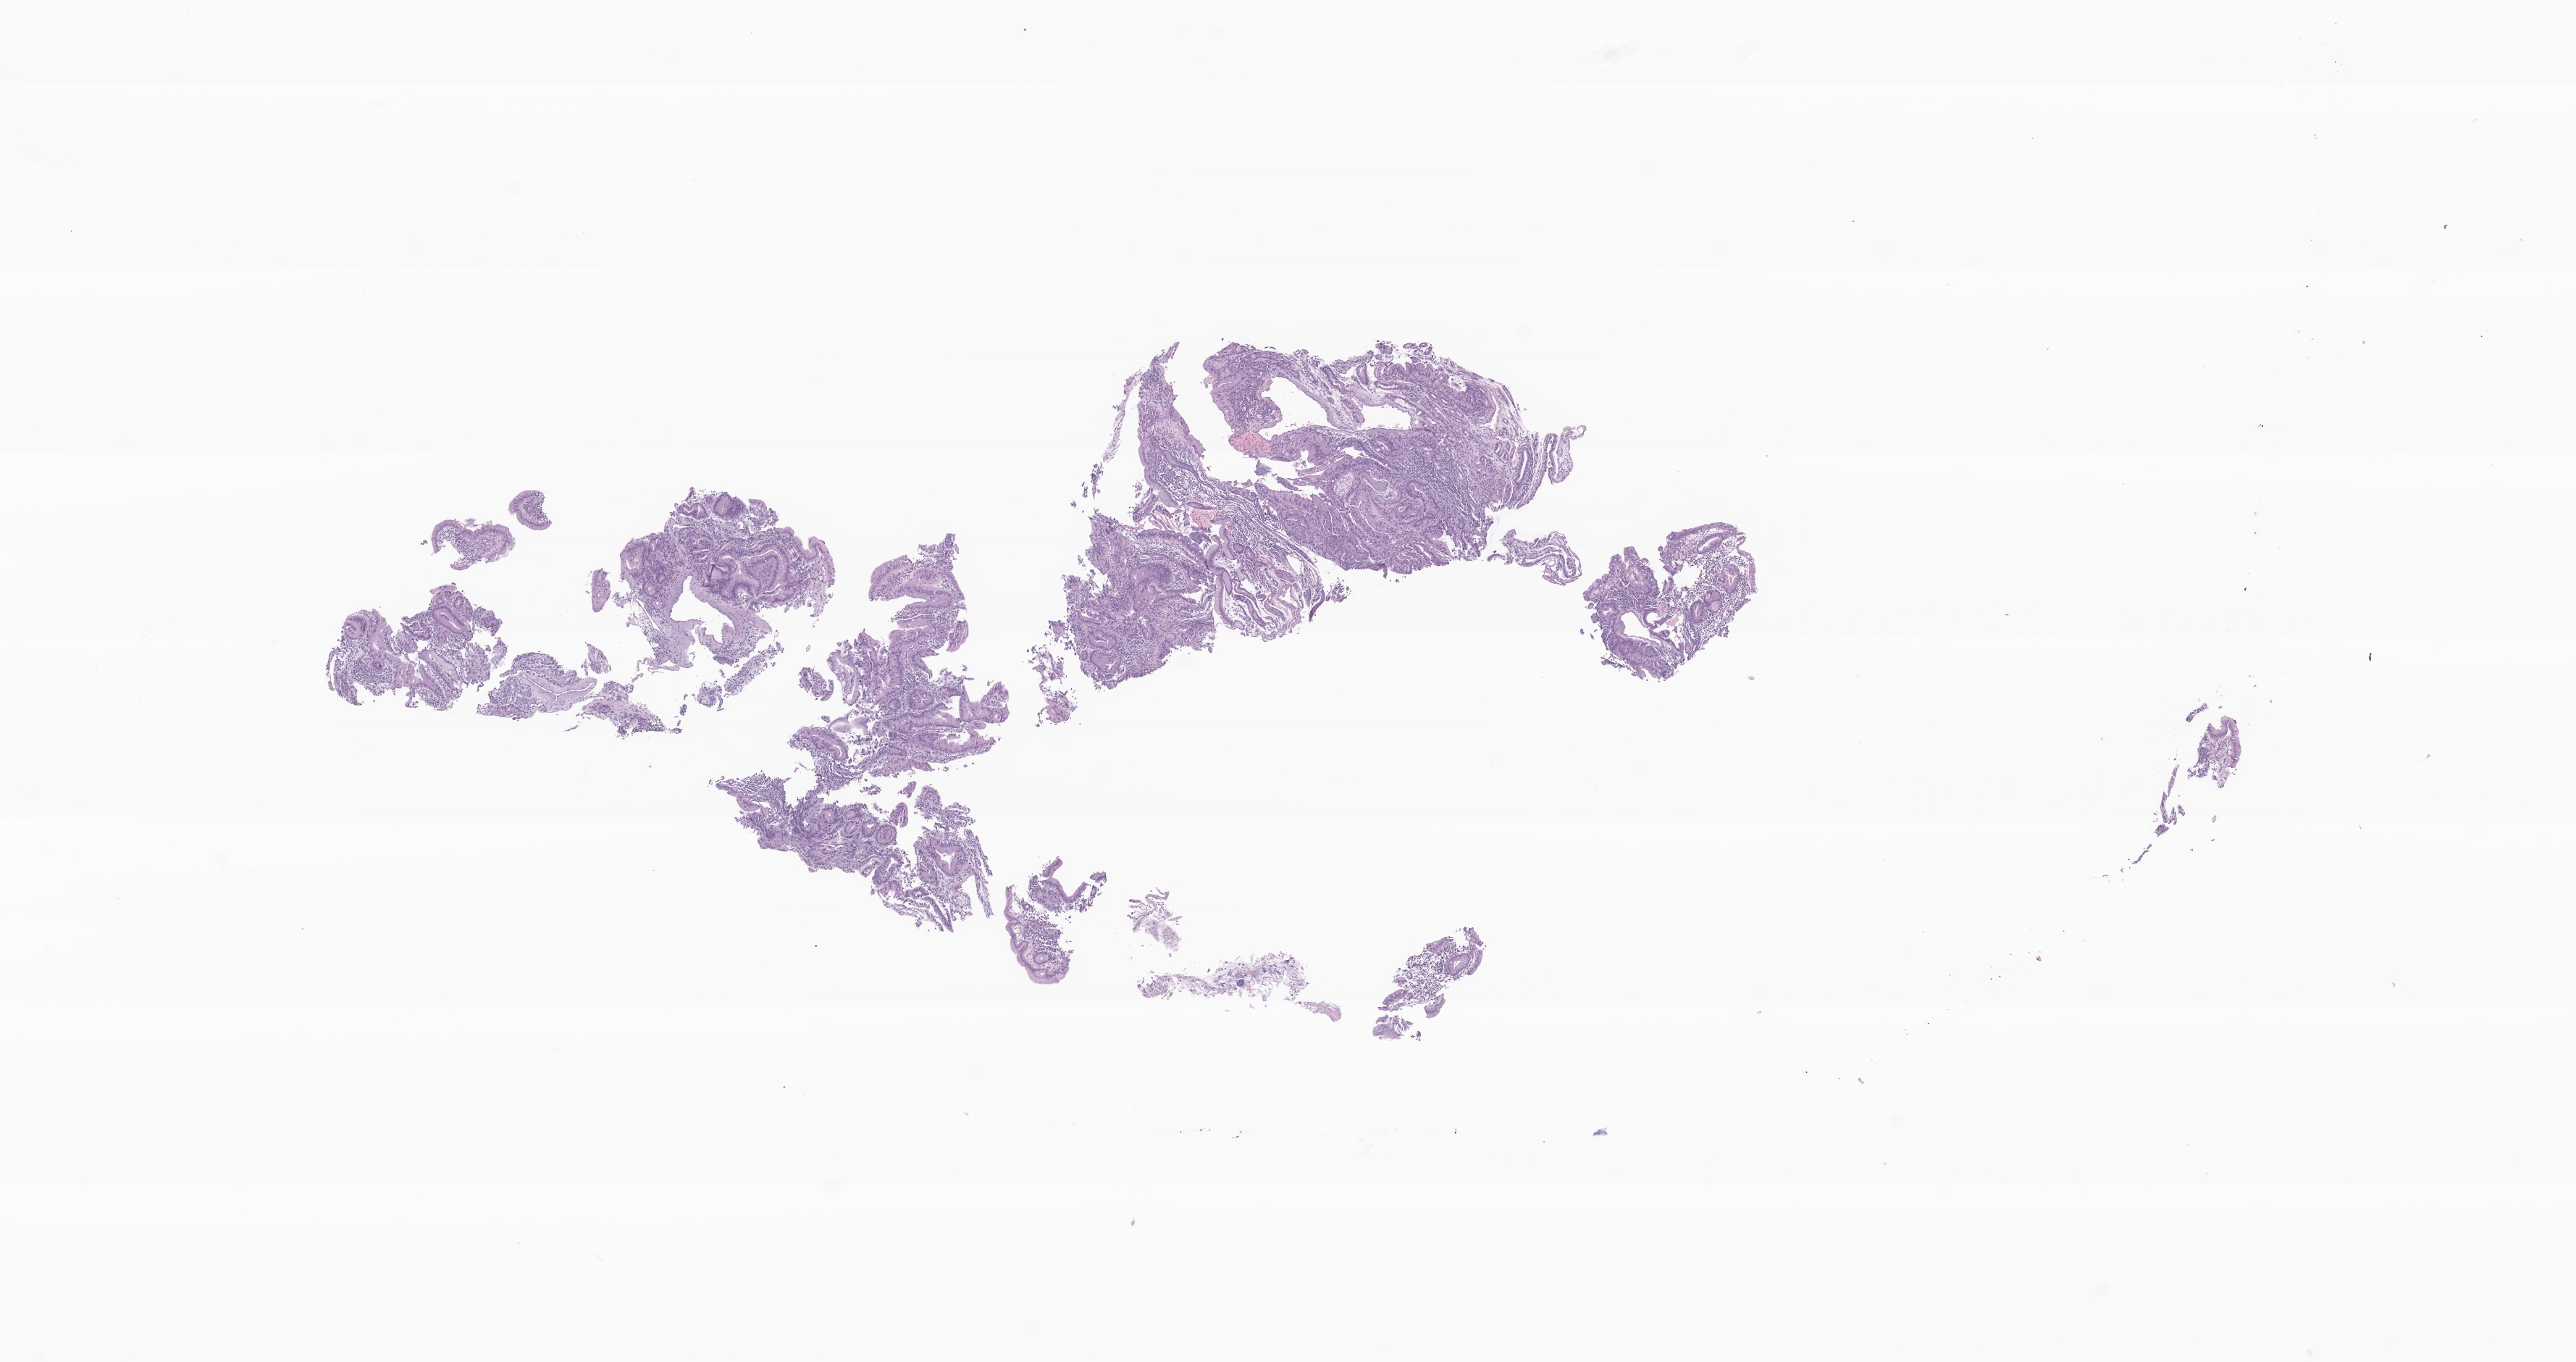
Whole-slide image, H&E stain of tumor tissue from the gastrointestinal tract — whole scanned area (about 15.0 x 7.9 mm) shown as a low-resolution overview, formalin-fixed, paraffin-embedded (FFPE) tissue. Female patient, age 234 months.
Recorded diagnosis: Adenocarcinoma, metastatic, NOS.